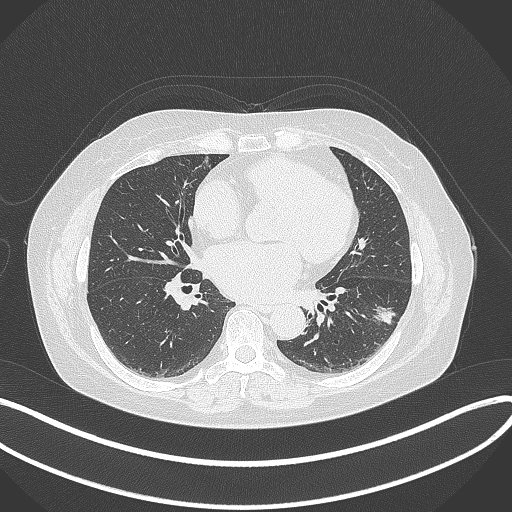
Chest CT, one axial slice; slice 162 of 373 in the series (ordered by position); 120 kVp; lung window (W 1500 / L -600 HU); 1 mm slice thickness; 512 × 512 image matrix, field of view 400 × 400 mm. Patient: female, 67 years. From the clinical record (not read from this slice): clinical TNM (as recorded): T1c N0 M0; histopathological grade: G2.
Annotated regions visible in this slice (bounding box drawn by a radiologist):
- lung tumour (recorded histology: adenocarcinoma): bounding box [x1, y1, x2, y2] px = [369, 298, 398, 330]